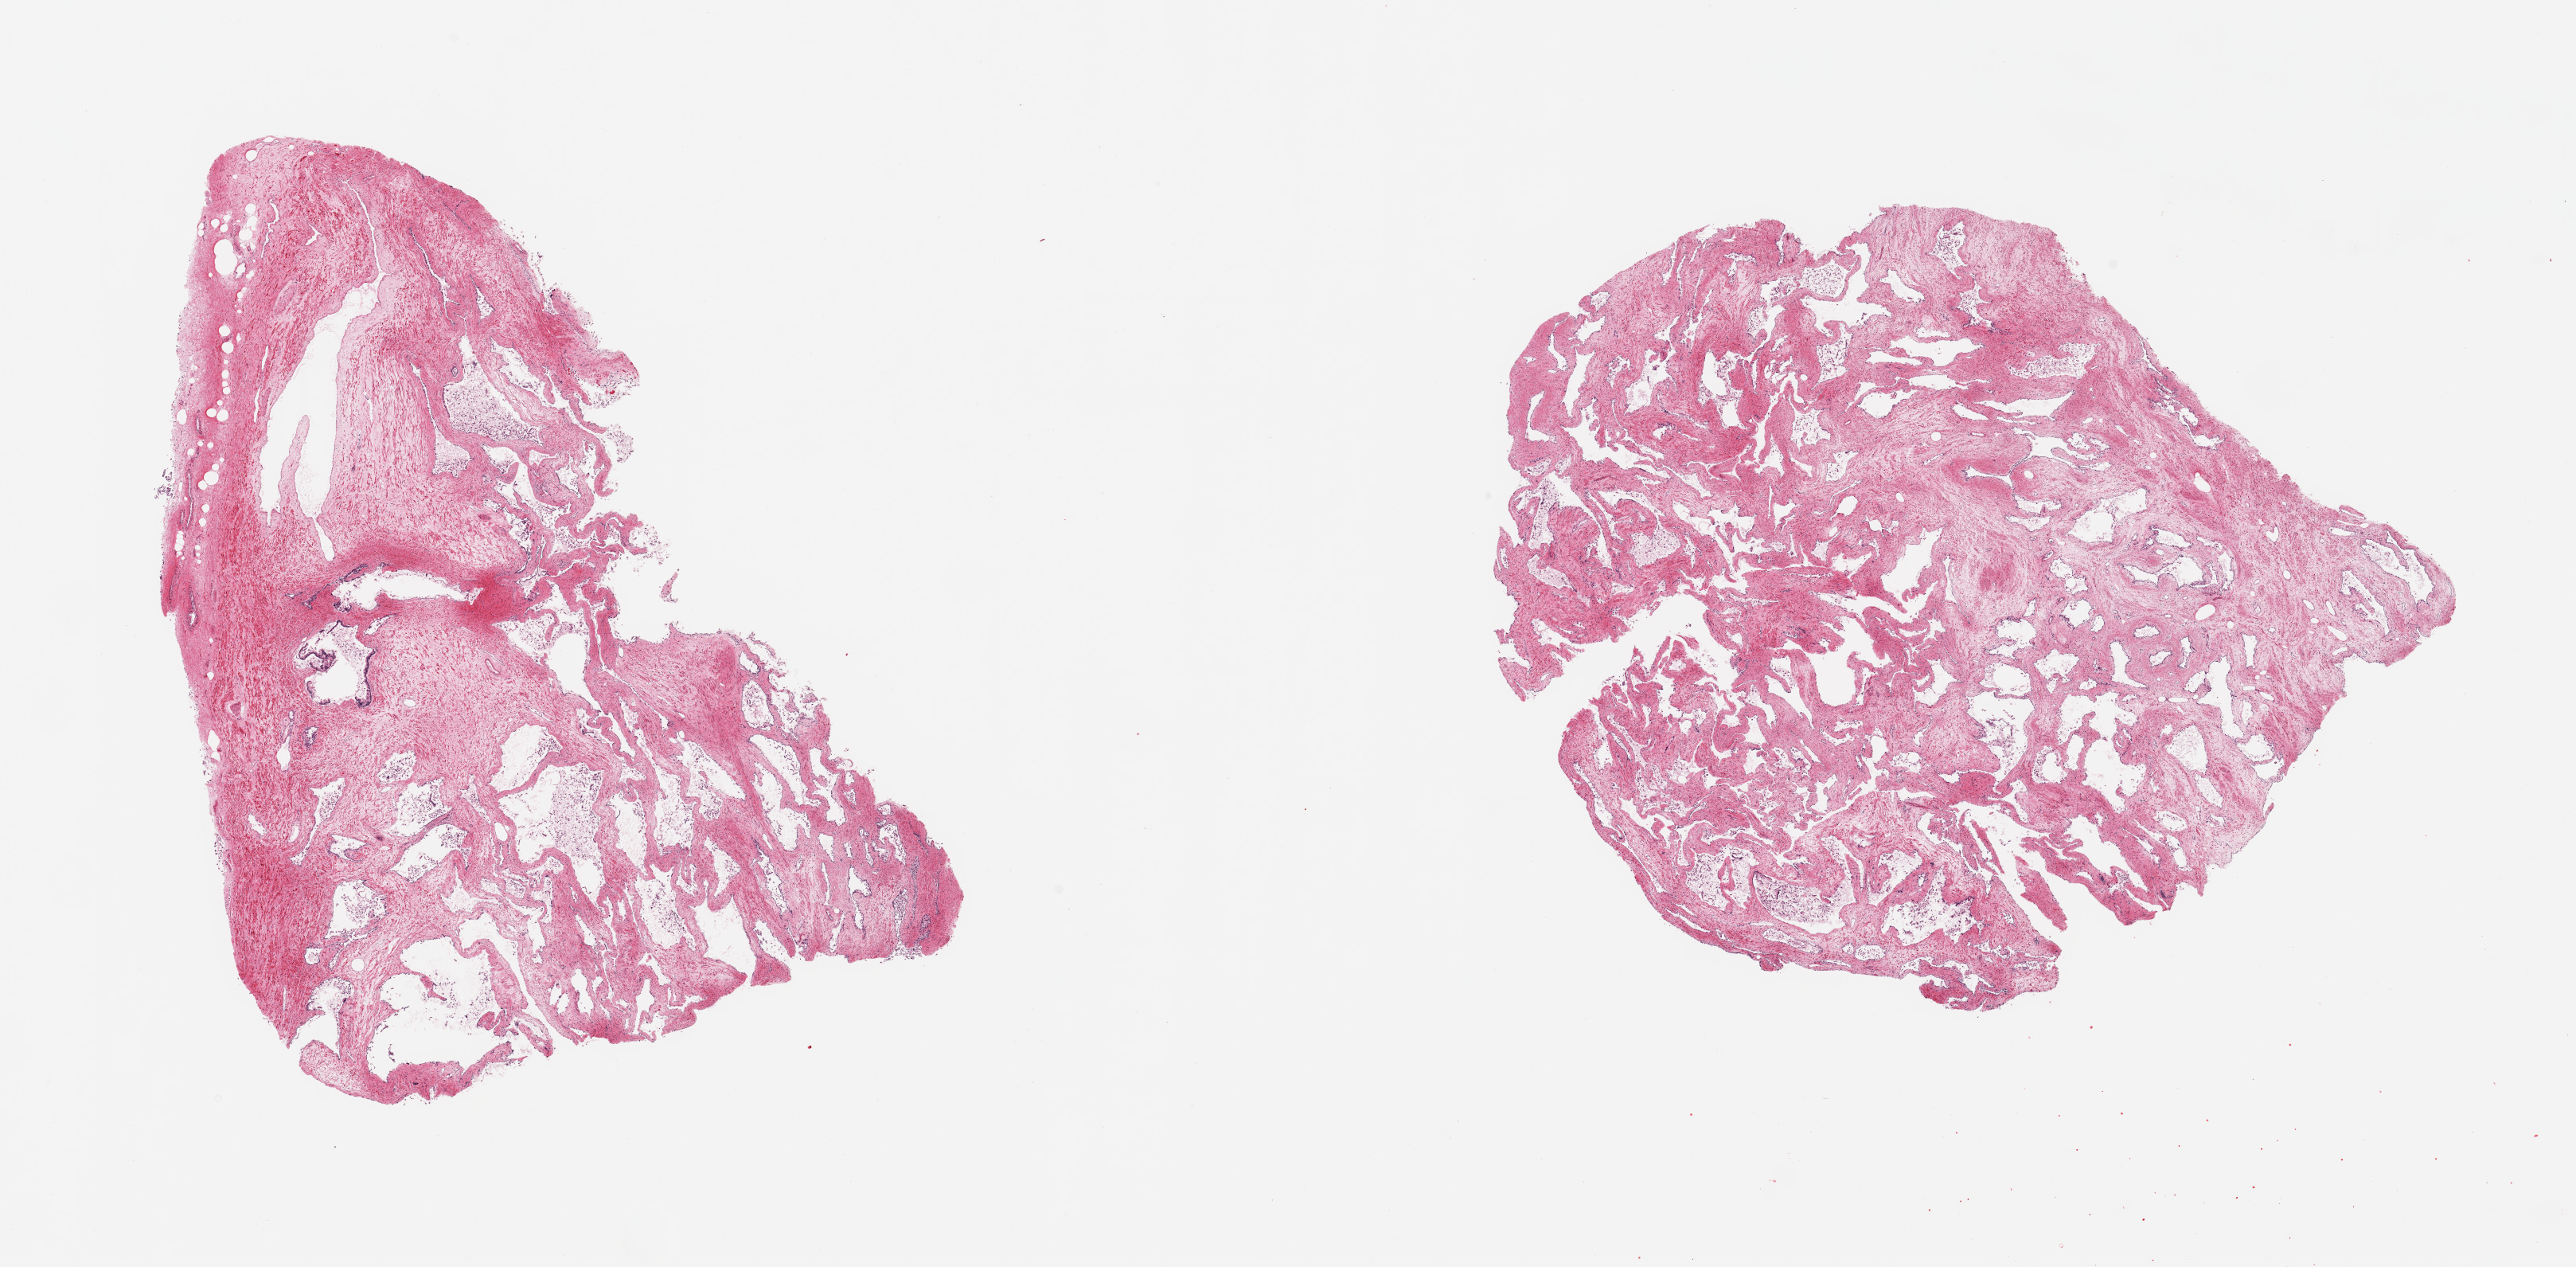
Whole-slide image, hematoxylin and eosin (H&E) stain — a low-resolution overview of the entire scanned area, about 25.6 x 12.6 mm, PAXgene-fixed, paraffin-embedded tissue, sampled site (target tissue): prostate, donor tissue sample. Donor: male.
- reviewer comment on this tissue sample: 2 pieces; autolyzed parenchyma and stroma